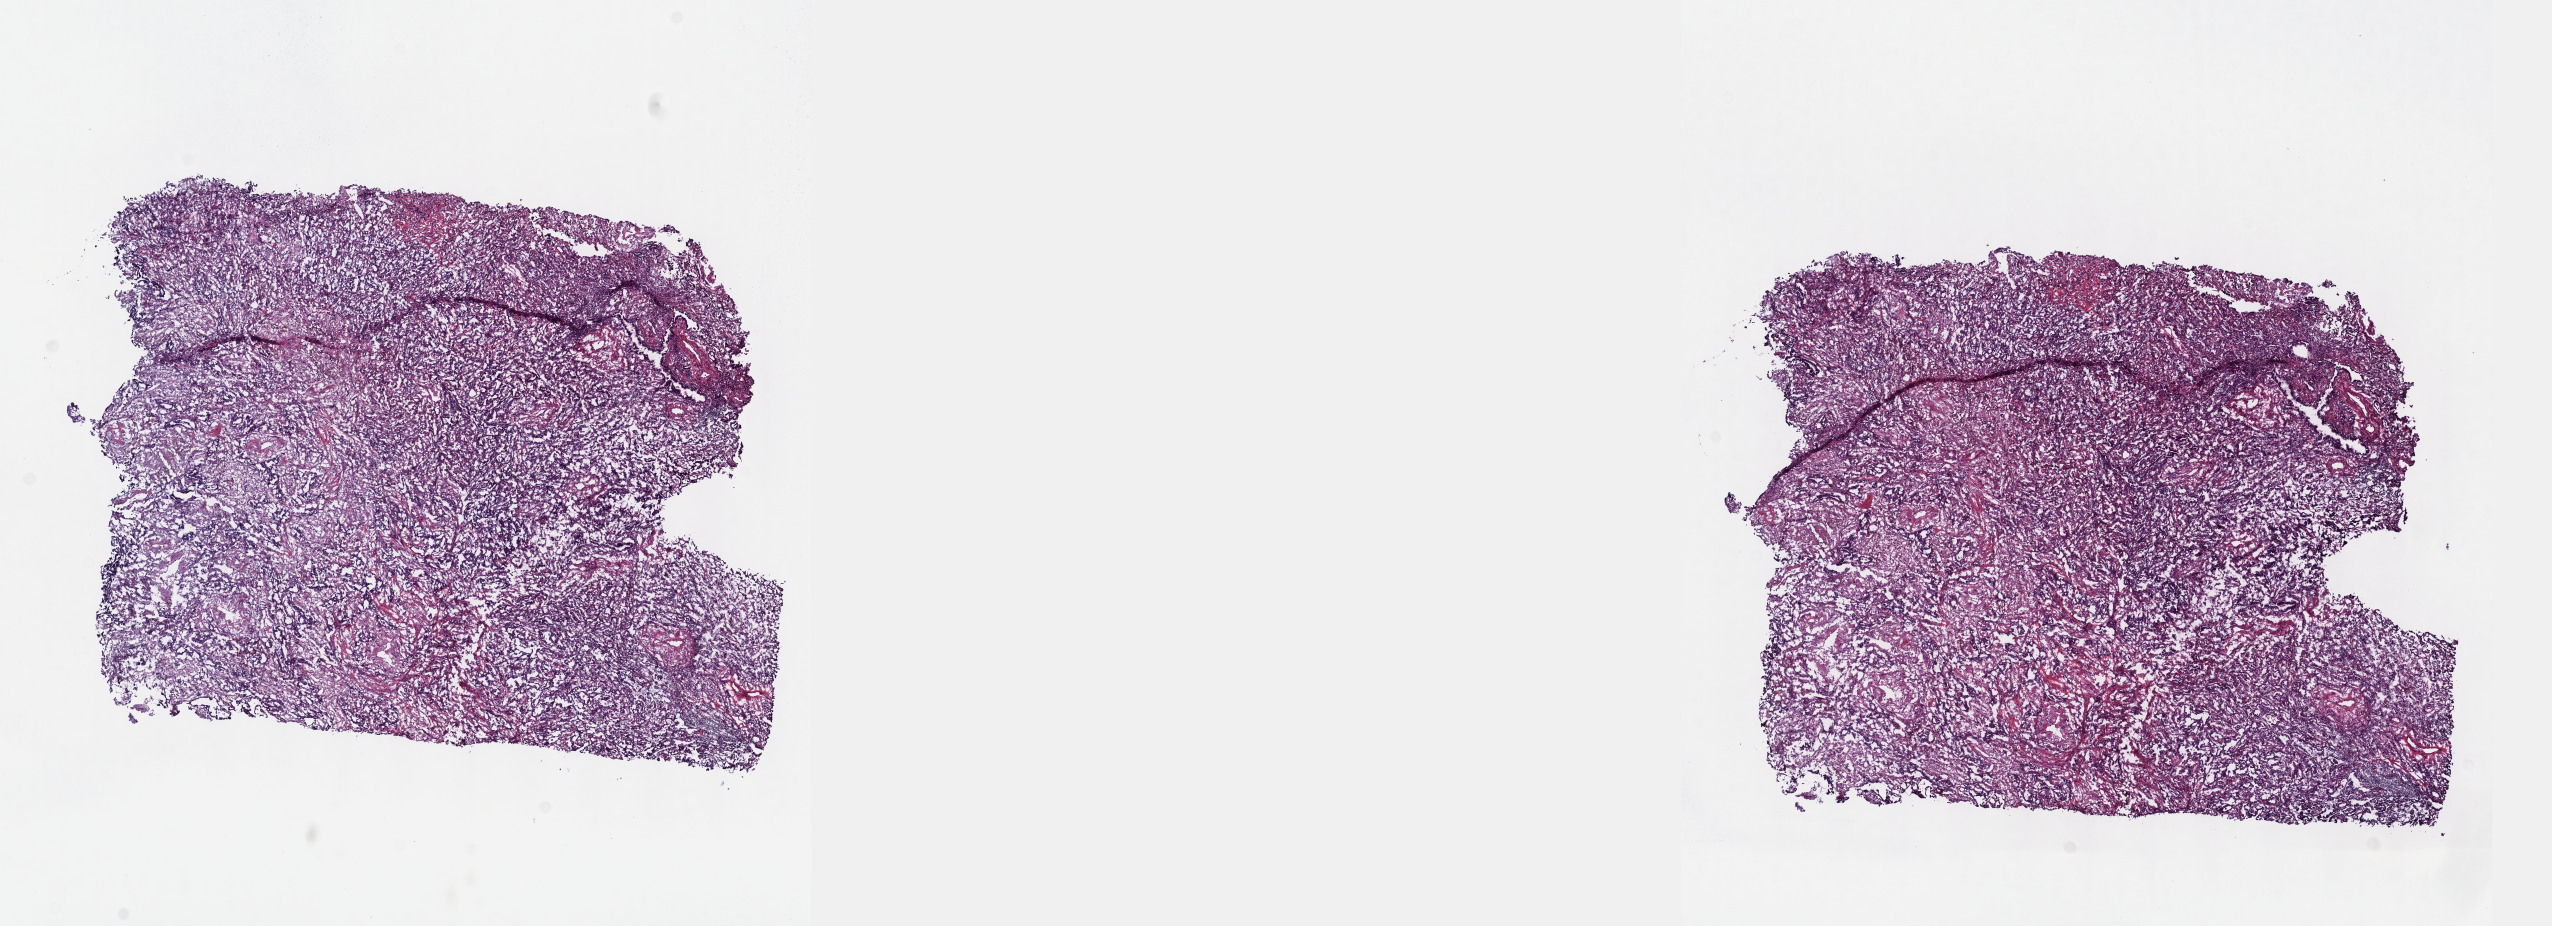
Hematoxylin and eosin (H&E) stained whole-slide image, whole scanned area (about 20.6 x 7.5 mm, acquisition: 40x scan) shown as a low-resolution overview. Frozen section from the top of the tissue portion. Sample: primary tumour, lung. Female patient; age at initial diagnosis 56 years. Slide review estimates, as recorded: tumour cells 60%, tumour nuclei 60%, normal cells 10%, stromal cells 25%, necrosis 5%. Inflammatory infiltration, as recorded: lymphocyte infiltration 2%, monocyte infiltration 2%, neutrophil infiltration 0%.
AJCC pathologic stage: IA (5th edition). Laterality: right. Diagnosis: Adenocarcinoma, NOS (lower lobe, lung).